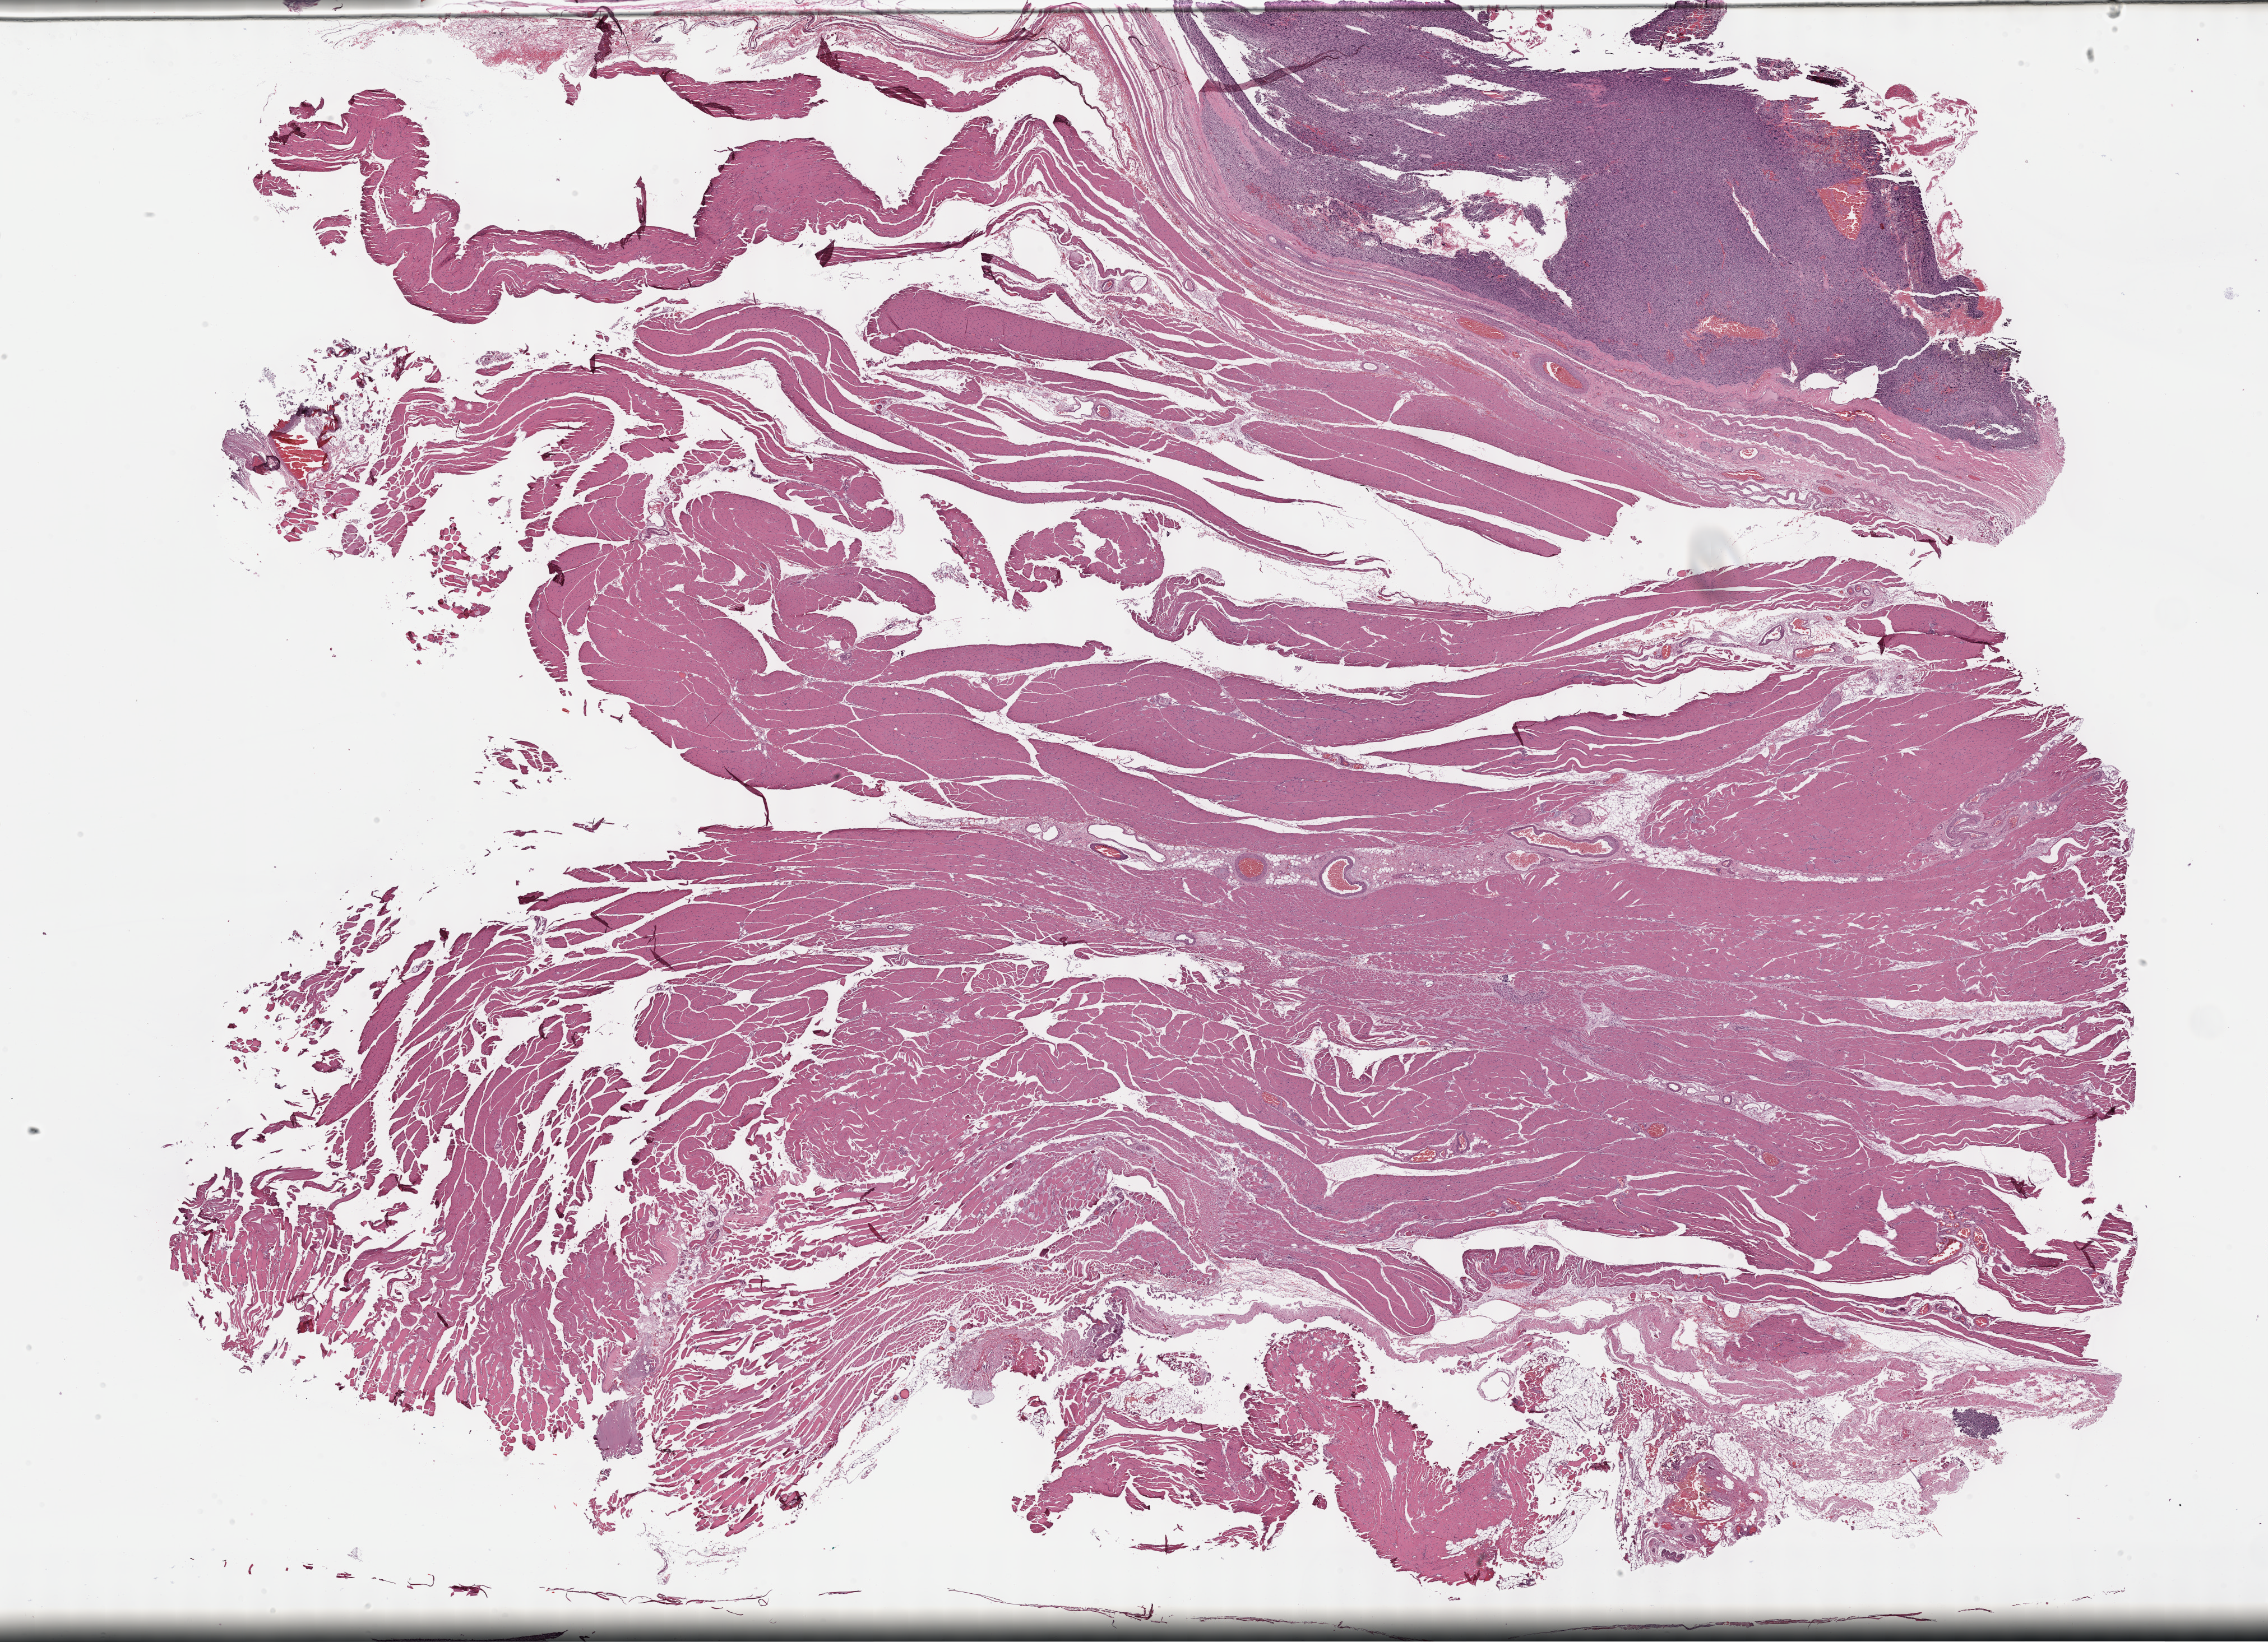
Whole-slide histology image, Hematoxylin and eosin (H&E) stained — whole scanned area (about 32.7 x 23.7 mm) shown as a low-resolution overview, FFPE section, primary tumour sample from the connective, subcutaneous and other soft tissues. Female patient; age at initial diagnosis 80 years.
Histologic diagnosis: Undifferentiated sarcoma (connective, subcutaneous and other soft tissues of lower limb and hip).